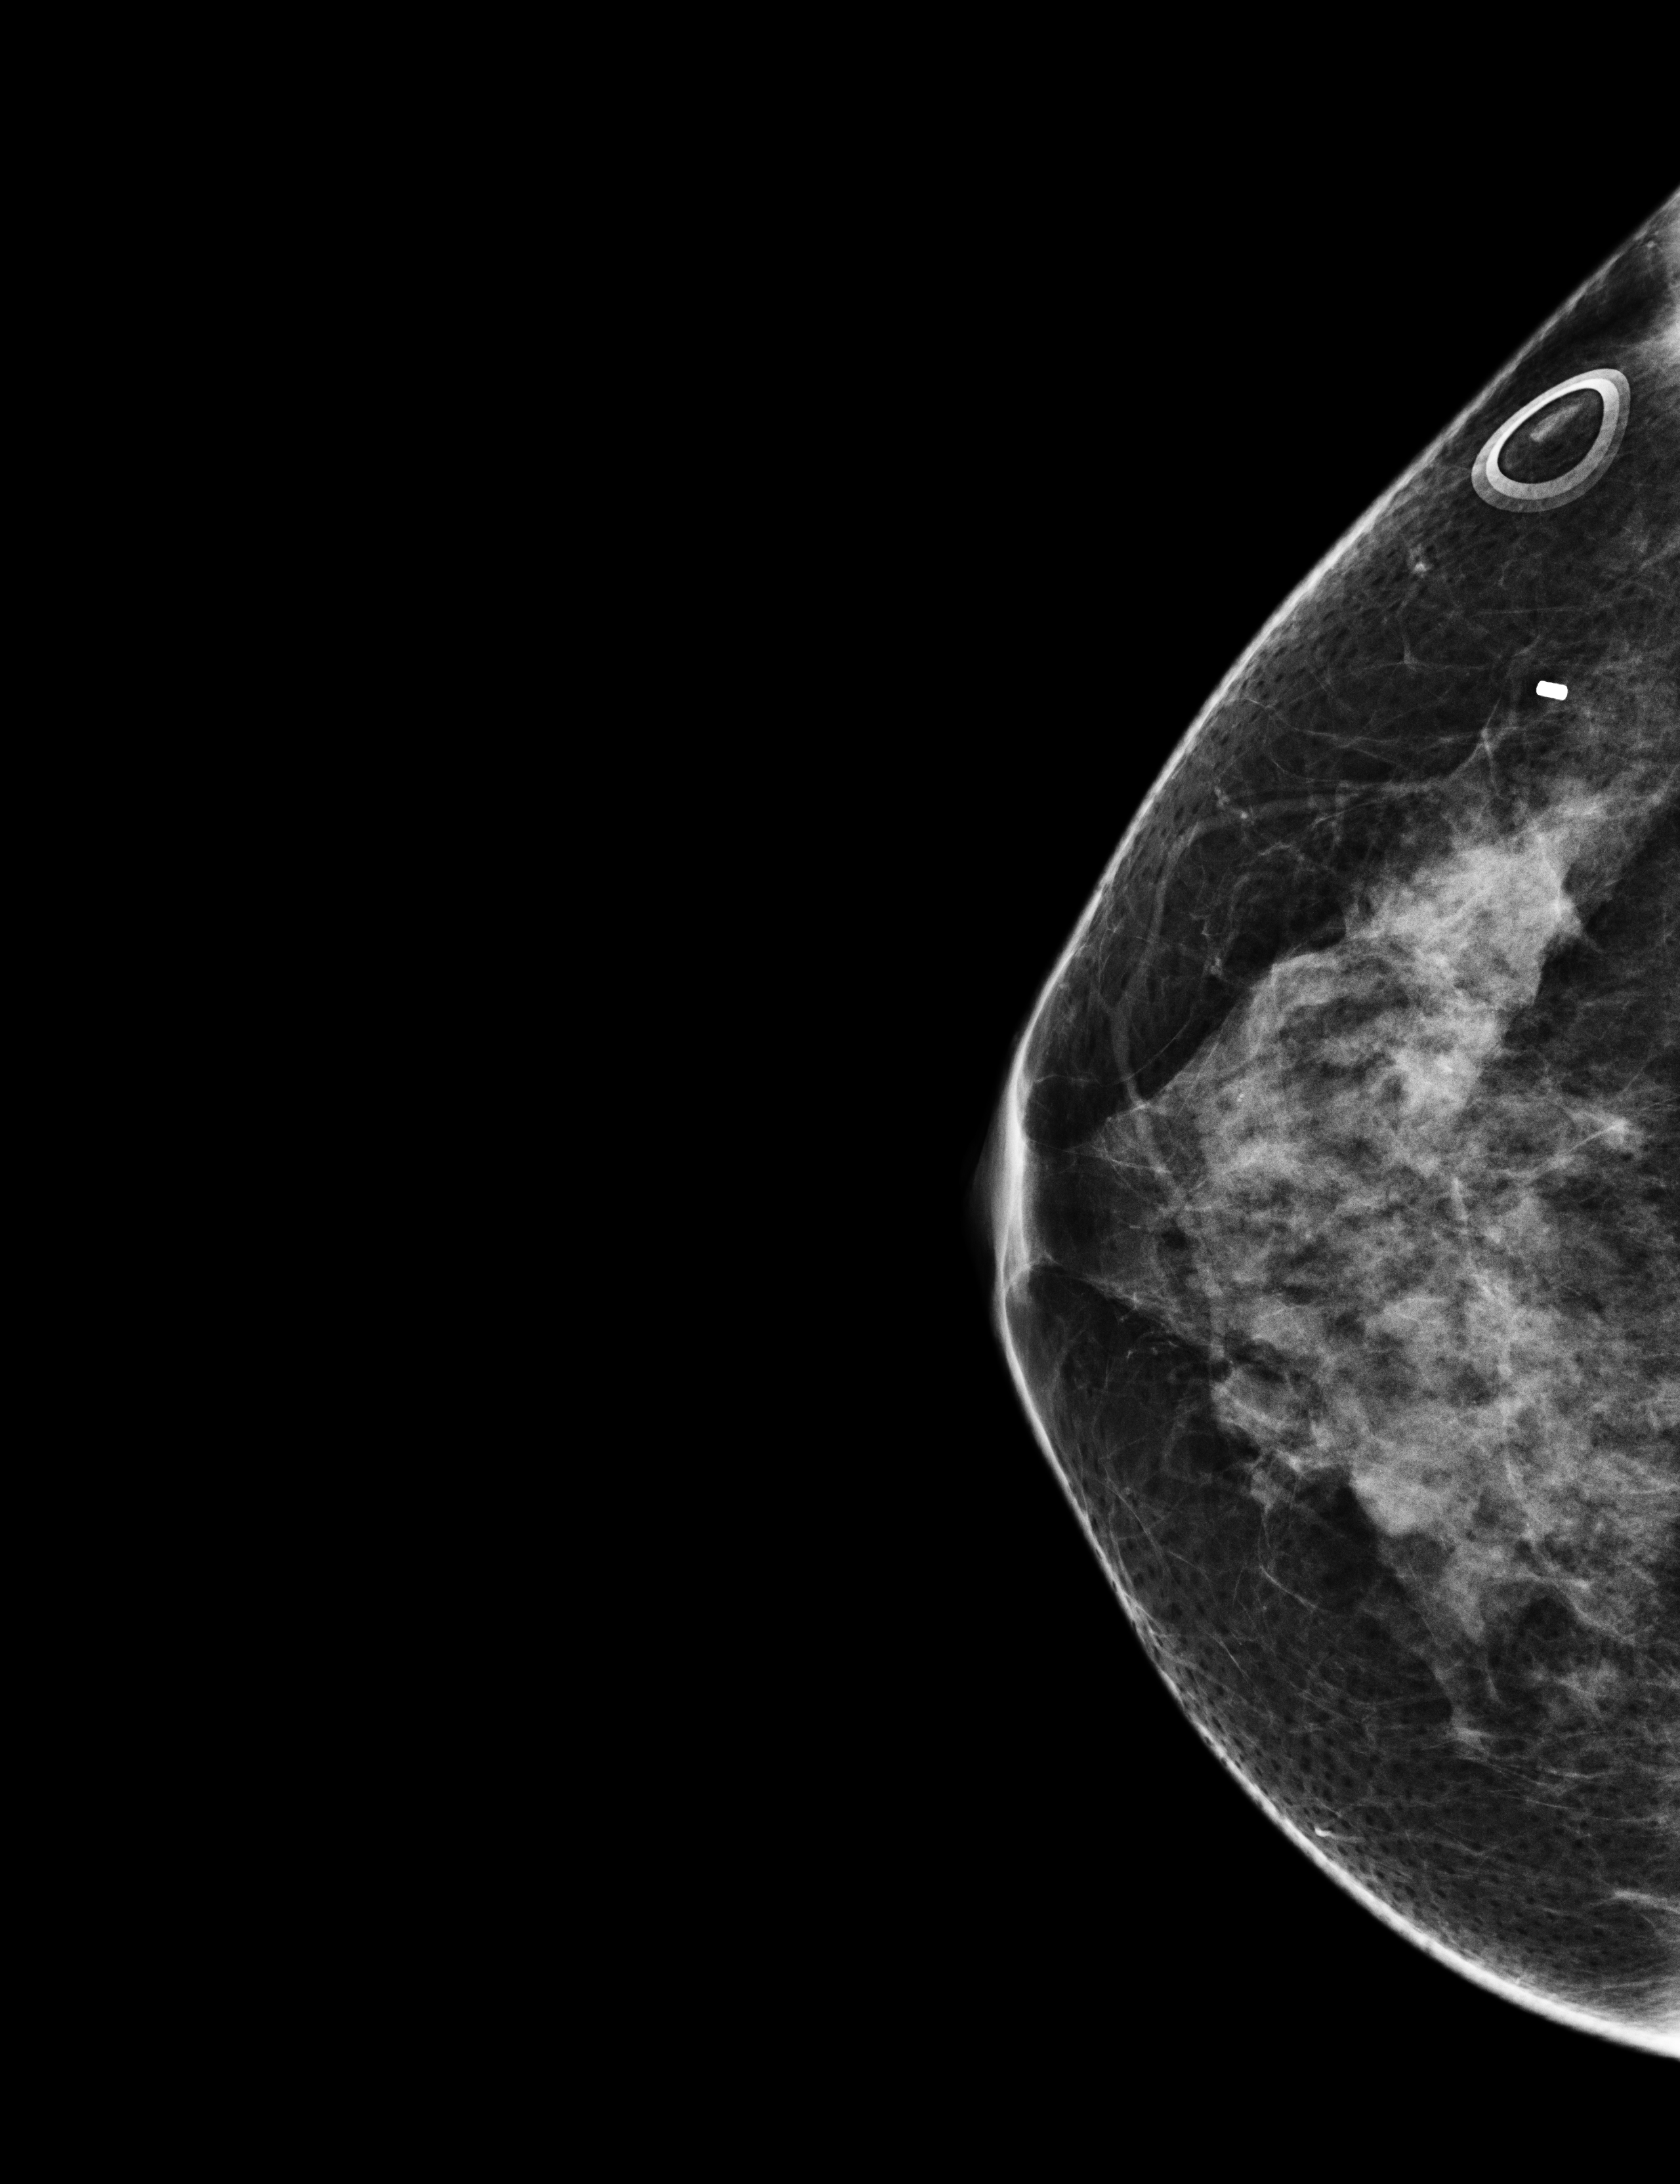
Screening examination, system: Selenia Dimensions. Patient aged 59 years (female).
Image type: full-field digital mammogram. Breast: right. Projection: cranio-caudal projection.